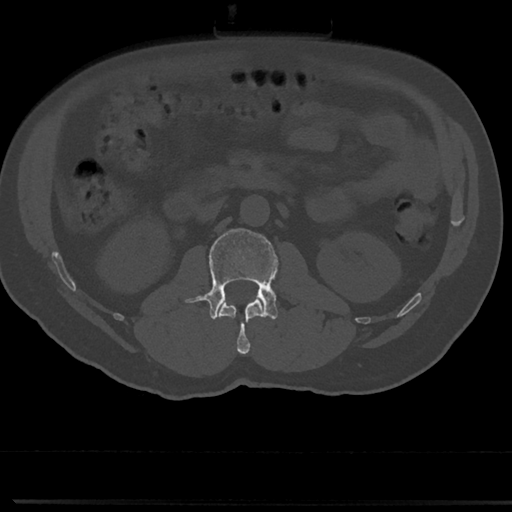
CT including the spine, one axial slice; position 36 of 817 along the scan axis; reconstruction kernel Br40s/3; bone window (W 1800 / L 400 HU); 0.5 mm slice thickness; 512 × 512 image matrix. Patient: male, 61 years. Case-level facts recorded for this patient, not image findings: primary cancer: prostate.
Outlined on this slice (semi-automatically segmented with operator editing):
- L1 vertebra: bounding box (x1, y1, x2, y2) in pixels: (219, 299, 263, 355)
- L2 vertebra: (191, 228, 278, 318)